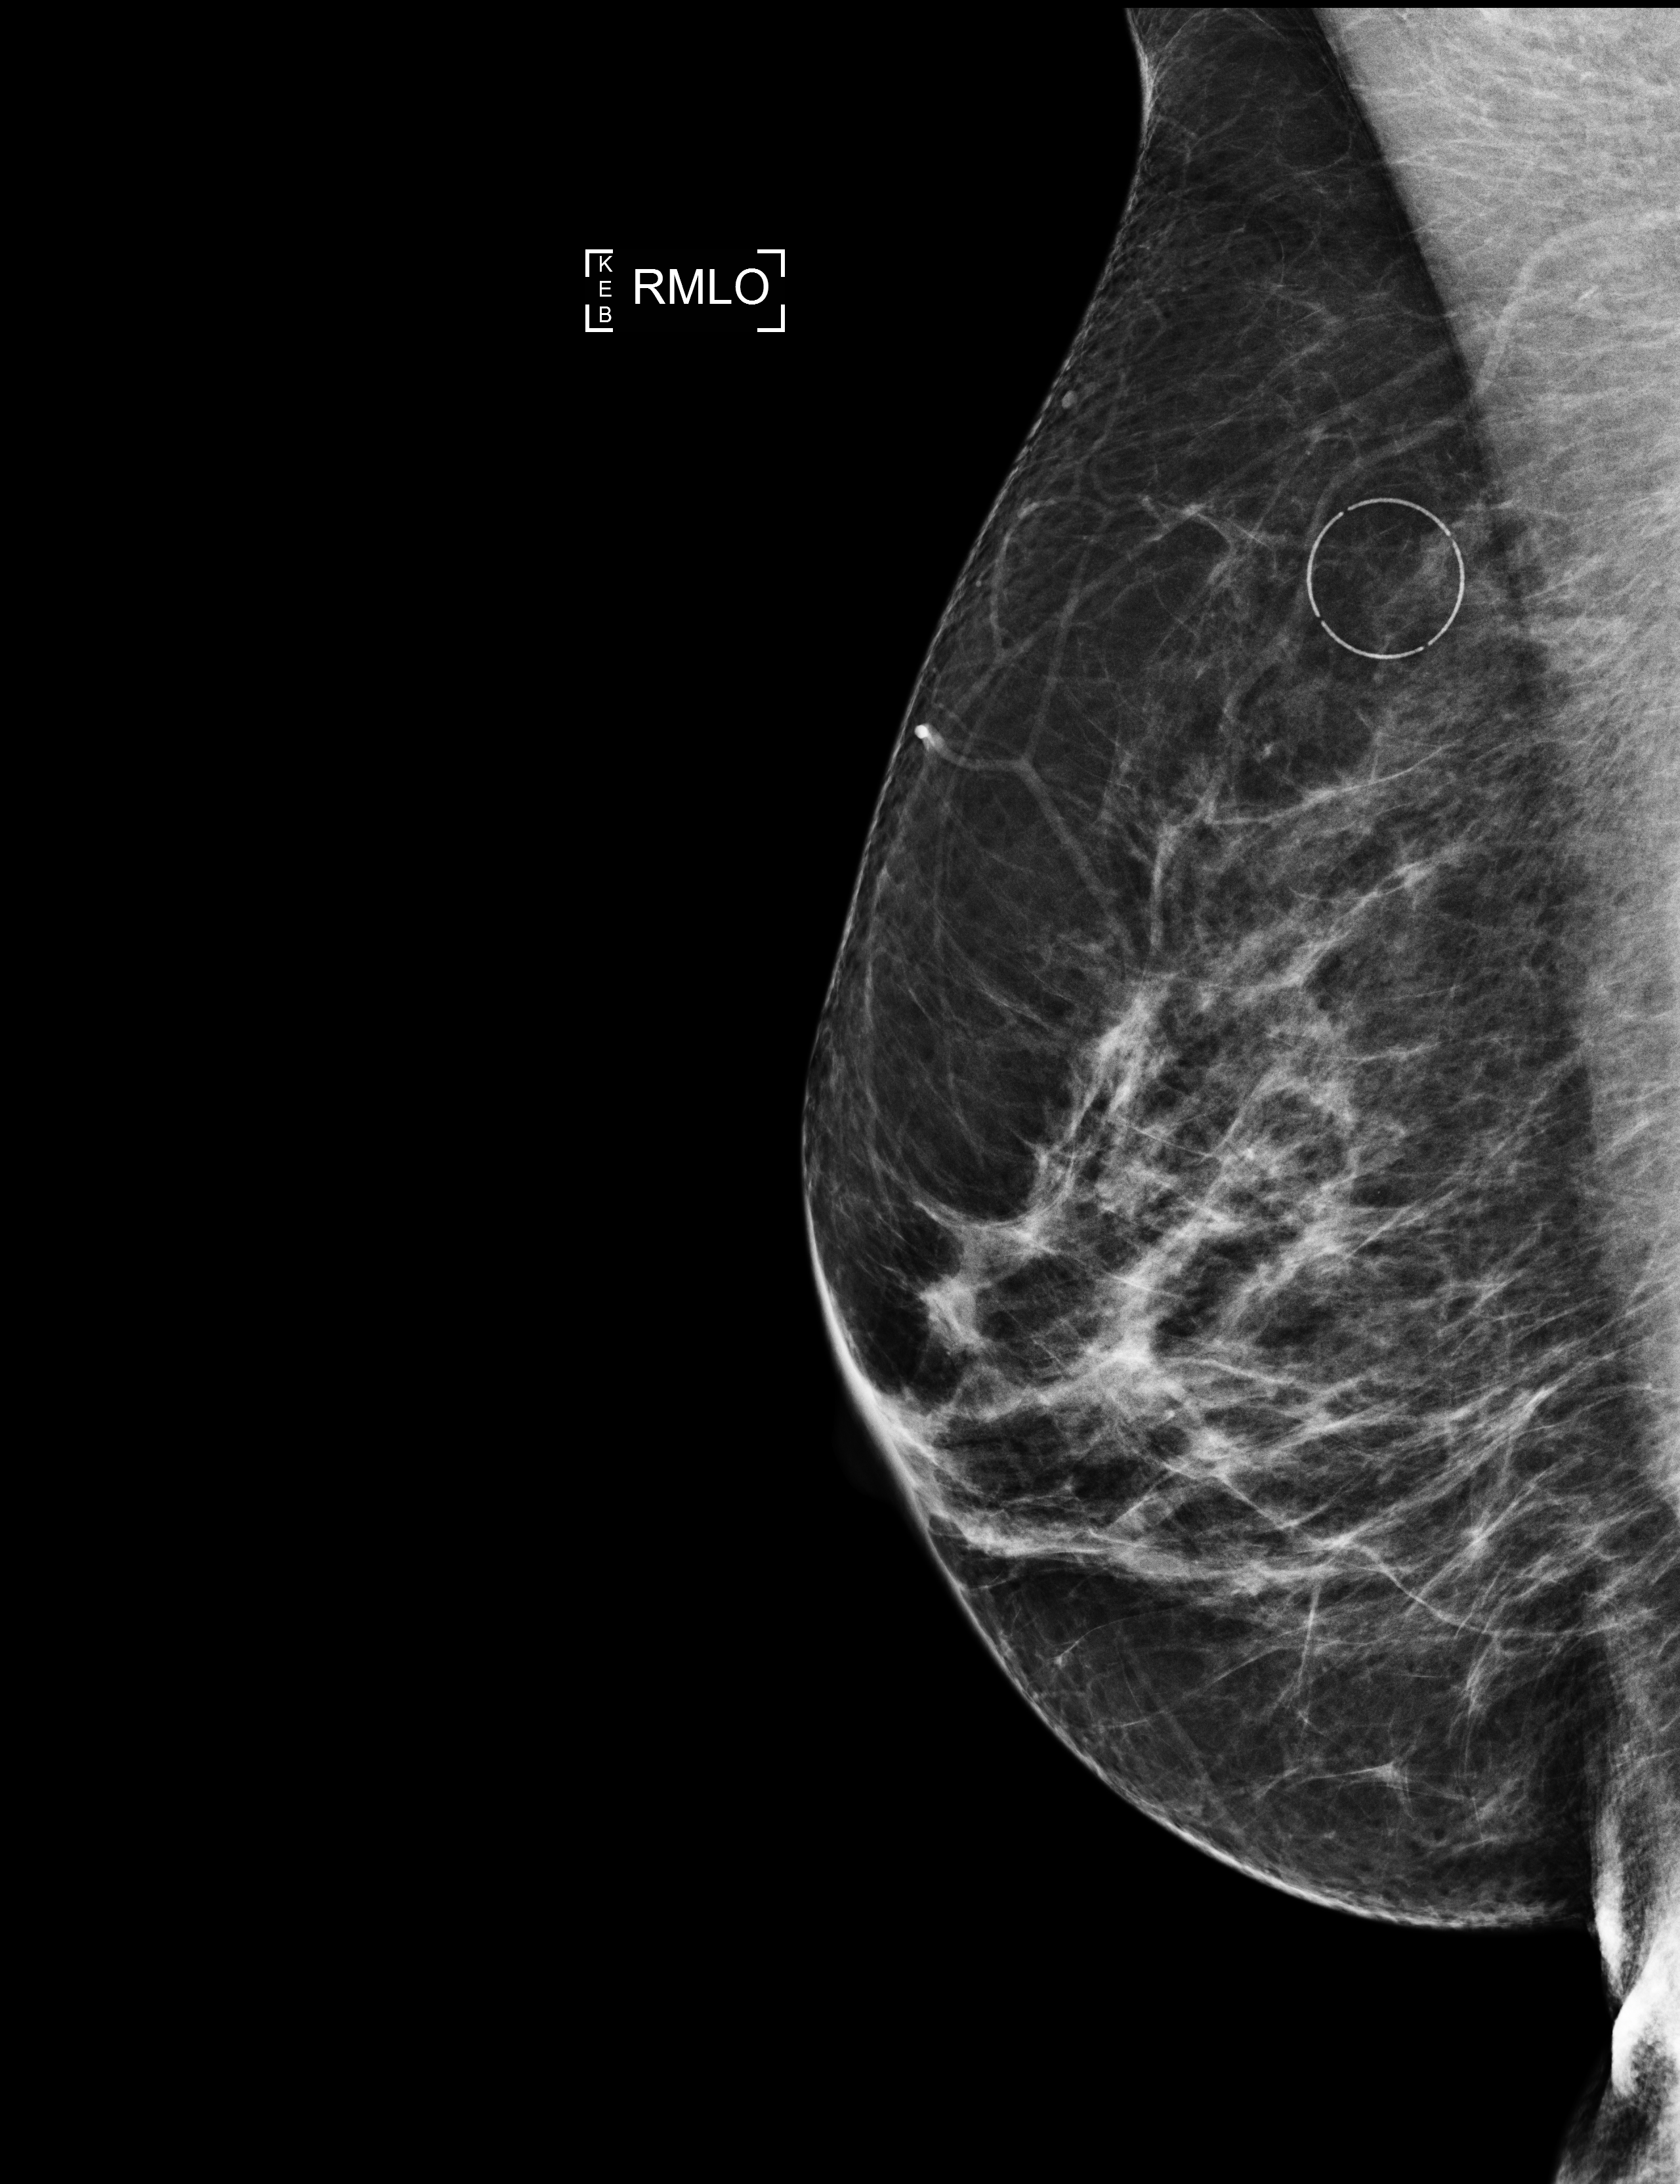
Annual screening mammography examination, compressed breast thickness 63 mm, system: Selenia Dimensions. Patient aged 60 years (female).
Image type: full-field digital mammogram. Breast: right. Projection: medio-lateral oblique projection. BI-RADS breast density category at the screening exam (both breasts, scale 1–4): 3. Final BI-RADS category for the screening round (tomosynthesis exam, both breasts): category 1. Recall: no recall after this screen.